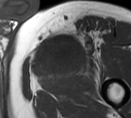
MRI of an extremity soft-tissue mass, one axial slice; position 52 of 55 along the scan axis; MR volume resampled by the dataset authors to the PET/CT grid (not the native acquisition matrix); 3.27 mm slice thickness; 131 × 118 image matrix. Male patient. From the clinical record (not read from this slice): histological type: pleiomorphic liposarcoma; grade: high; site of the primary tumour: left thigh.
Structures marked on this image (expert contour drawn on MRI and transferred to this co-registered scan by the dataset authors):
- gross tumour volume including surrounding oedema: bounding box [x1, y1, x2, y2] px = [32, 29, 97, 76]
- gross tumour volume (mass): [32, 34, 76, 67]